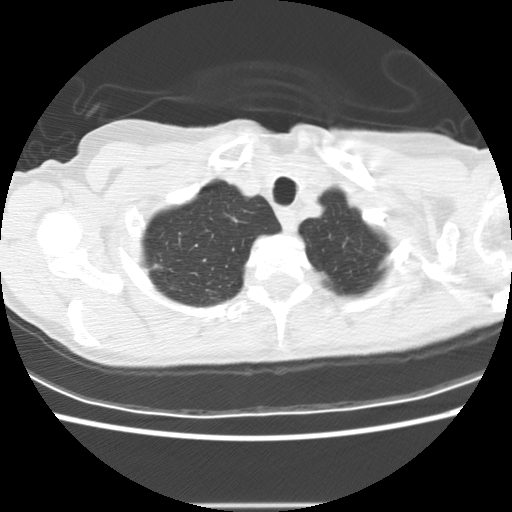
Chest CT (low-dose screening protocol), one axial image, second screening round (one year after baseline), lung window (W 1500 / L -600 HU), standard (soft-tissue) reconstruction kernel (STANDARD), slice 14 of 166 in the series. Female, age 58 years at enrolment. Current smoker at enrolment.
• Lesion marked by an expert reader, bounding box [x1, y1, x2, y2] px = [137, 252, 181, 288].
• The screening reader recorded 2 non-calcified nodules or masses ≥4 mm on this exam (right upper lobe, right upper lobe); which of them this box marks is not recorded.
• Later outcome: lung cancer diagnosed 434 days after this screen (after the third annual screen) — bronchiolo-alveolar adenocarcinoma, NOS, right upper lobe, well differentiated (G1), stage IA (AJCC 6th edition), 8 mm at pathology.